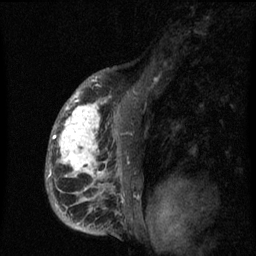
Breast MRI (dynamic contrast-enhanced), one sagittal slice; position 44 of 60 along the scan axis; dynamic contrast-enhanced series, image 2 of 3 at this slice position (ordered by acquisition); 1.5 T; TE 4.2 ms, TR 8 ms; 2 mm slice thickness; 256 × 256 image matrix, field of view 190 × 190 mm. Patient: female, 50 years.
Annotated regions visible in this slice (semi-automatically segmented with operator editing):
- analysis volume of interest (the breast-tissue region the enhancement analysis was run in; not a lesion): bounding box [x1, y1, x2, y2] px = [45, 90, 142, 216]
- tumour enhancement mask (voxels above the 70 % enhancement threshold inside the analysis volume of interest): [48, 90, 123, 202]